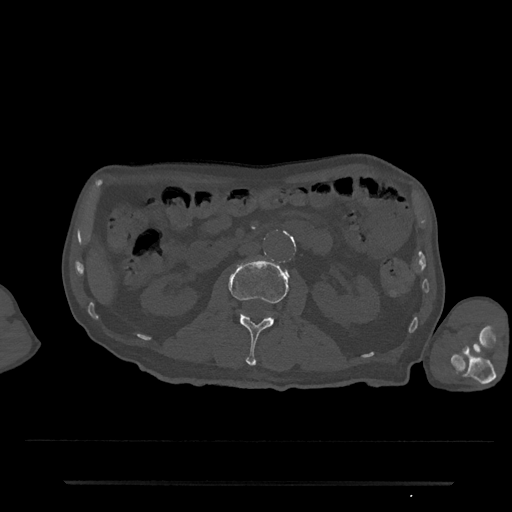
CT including the spine, one axial slice. Position 45 of 797 along the scan axis. Bone window (W 1800 / L 400 HU). 0.5 mm slice thickness. 512 × 512 image matrix, field of view 427 × 427 mm. Male patient, age 74 years. From the clinical record (not read from this slice): primary cancer: prostate.
Structures marked on this image (semi-automatically segmented with operator editing):
- L2 vertebra: bounding box <228,258,289,366> (left, top, right, bottom; pixels)